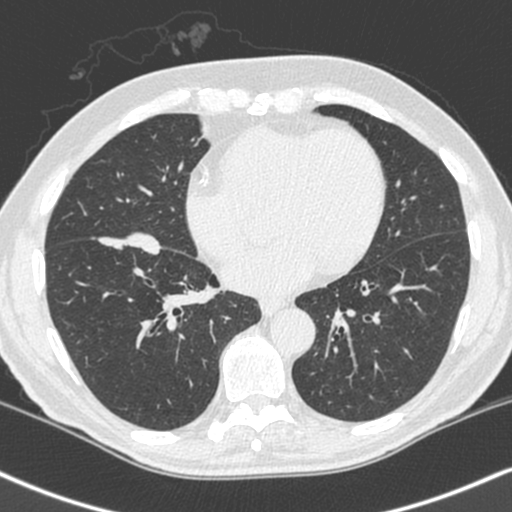
Axial slice from a low-dose chest CT screening exam; first (baseline) screen; lung window (W 1500 / L -600 HU); 1.3 mm slice thickness; standard (soft-tissue) reconstruction kernel (C); 120 kVp; slice 141 of 248 in the series. Male, age 68 years at enrolment. Current smoker at enrolment.
• Lesion marked by an expert reader, box from (x=89, y=228) to (x=164, y=299) px.
• Reader record for this screening exam (exam-level; its link to the box is not recorded): non-calcified nodule or mass ≥4 mm, right lower lobe, 34 × 17 mm, smooth margins, soft tissue attenuation.
• Official screen result: positive, change unspecified: nodule(s) >= 4 mm or enlarging nodule(s), mass(es), or other non-specific abnormalities suspicious for lung cancer.